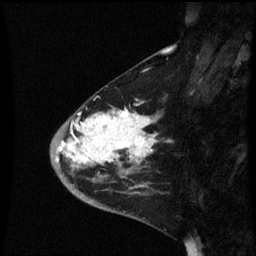
Breast MRI (dynamic contrast-enhanced), one sagittal slice; position 22 of 60 along the scan axis; dynamic contrast-enhanced series, image 2 of 3 at this slice position (ordered by acquisition); 1.5 T; TE 4.2 ms, TR 8.4 ms; 2.3 mm slice thickness; 256 × 256 image matrix, field of view 200 × 200 mm. Female patient, age 46 years. From the clinical record (not read from this slice): setting: breast cancer imaged before/during neoadjuvant chemotherapy; receptor status: HER2-positive.
Annotated regions visible in this slice (semi-automatically segmented with operator editing):
- analysis volume of interest (the breast-tissue region the enhancement analysis was run in; not a lesion): bounding box <50,96,158,187> (left, top, right, bottom; pixels)
- tumour enhancement mask (voxels above the 70 % enhancement threshold inside the analysis volume of interest): <56,108,155,165>